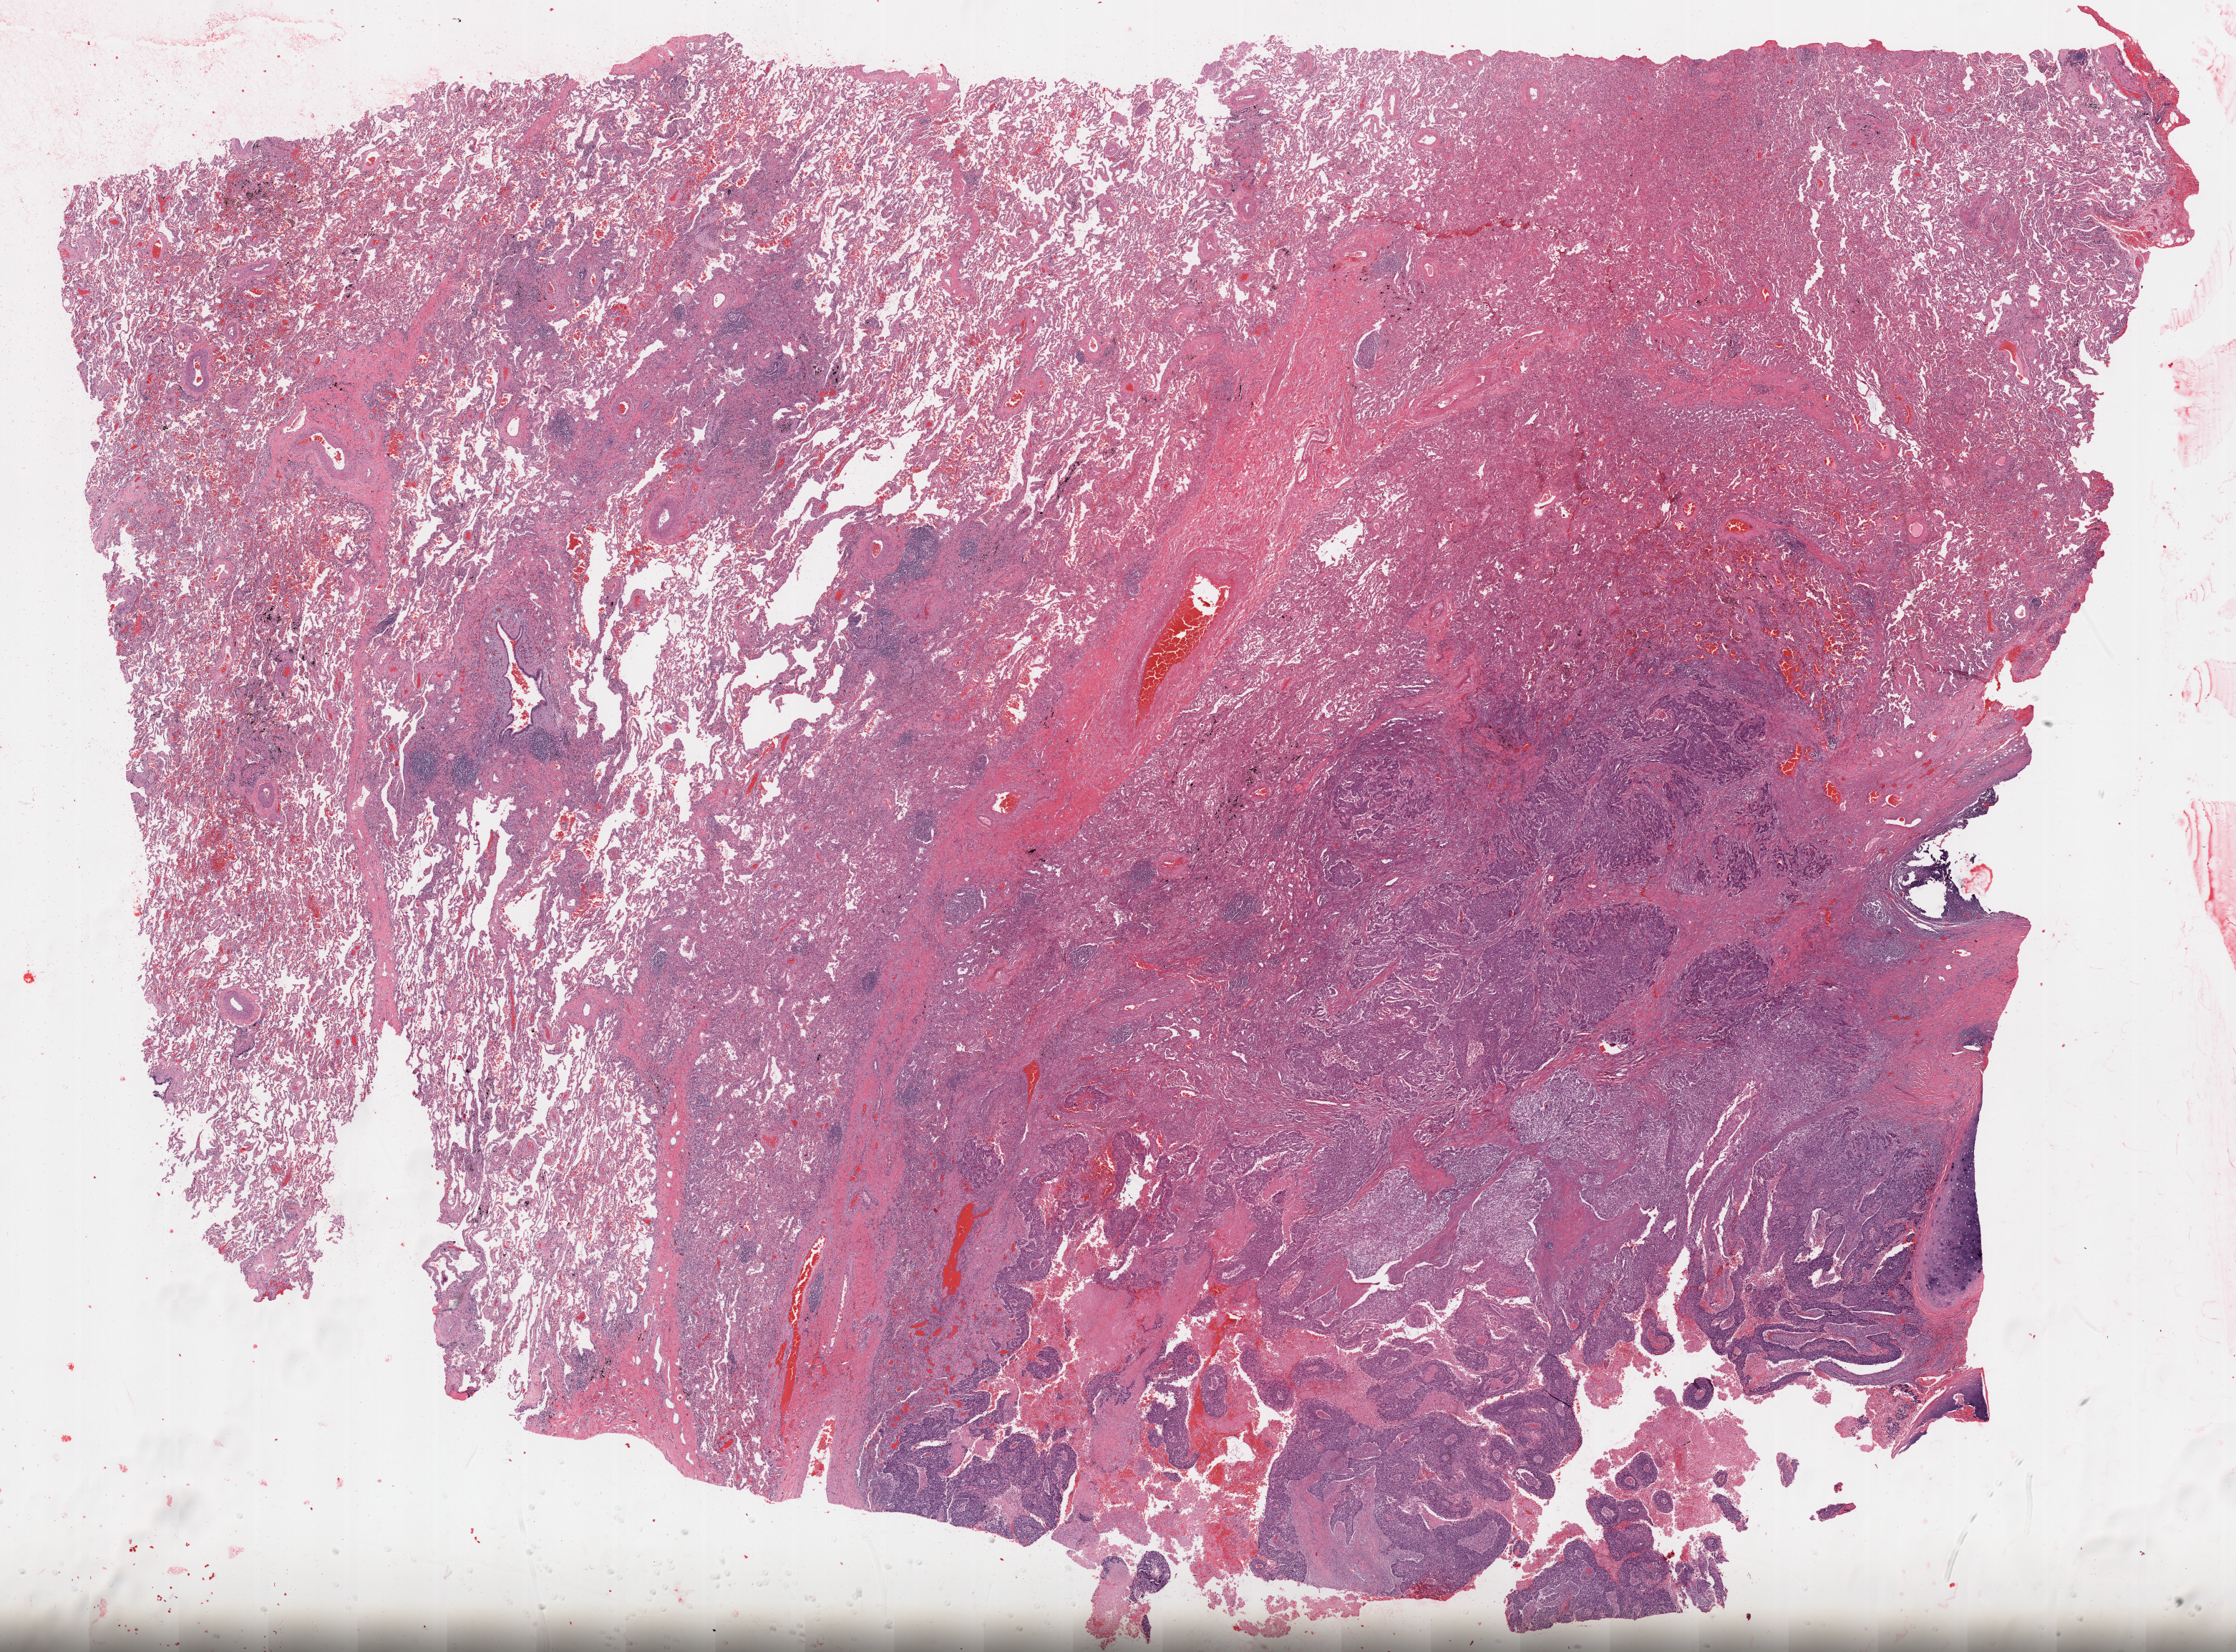
H&E-stained whole-slide image, shown as a low-resolution overview of the whole scanned area (about 25.1 x 18.6 mm). Formalin-fixed paraffin-embedded (FFPE) diagnostic section. Primary tumour sample from the lung. Male, age 66 years at initial diagnosis.
- histologic diagnosis: Squamous cell carcinoma, NOS (upper lobe, lung)
- AJCC pathologic stage: IIB
- laterality: right